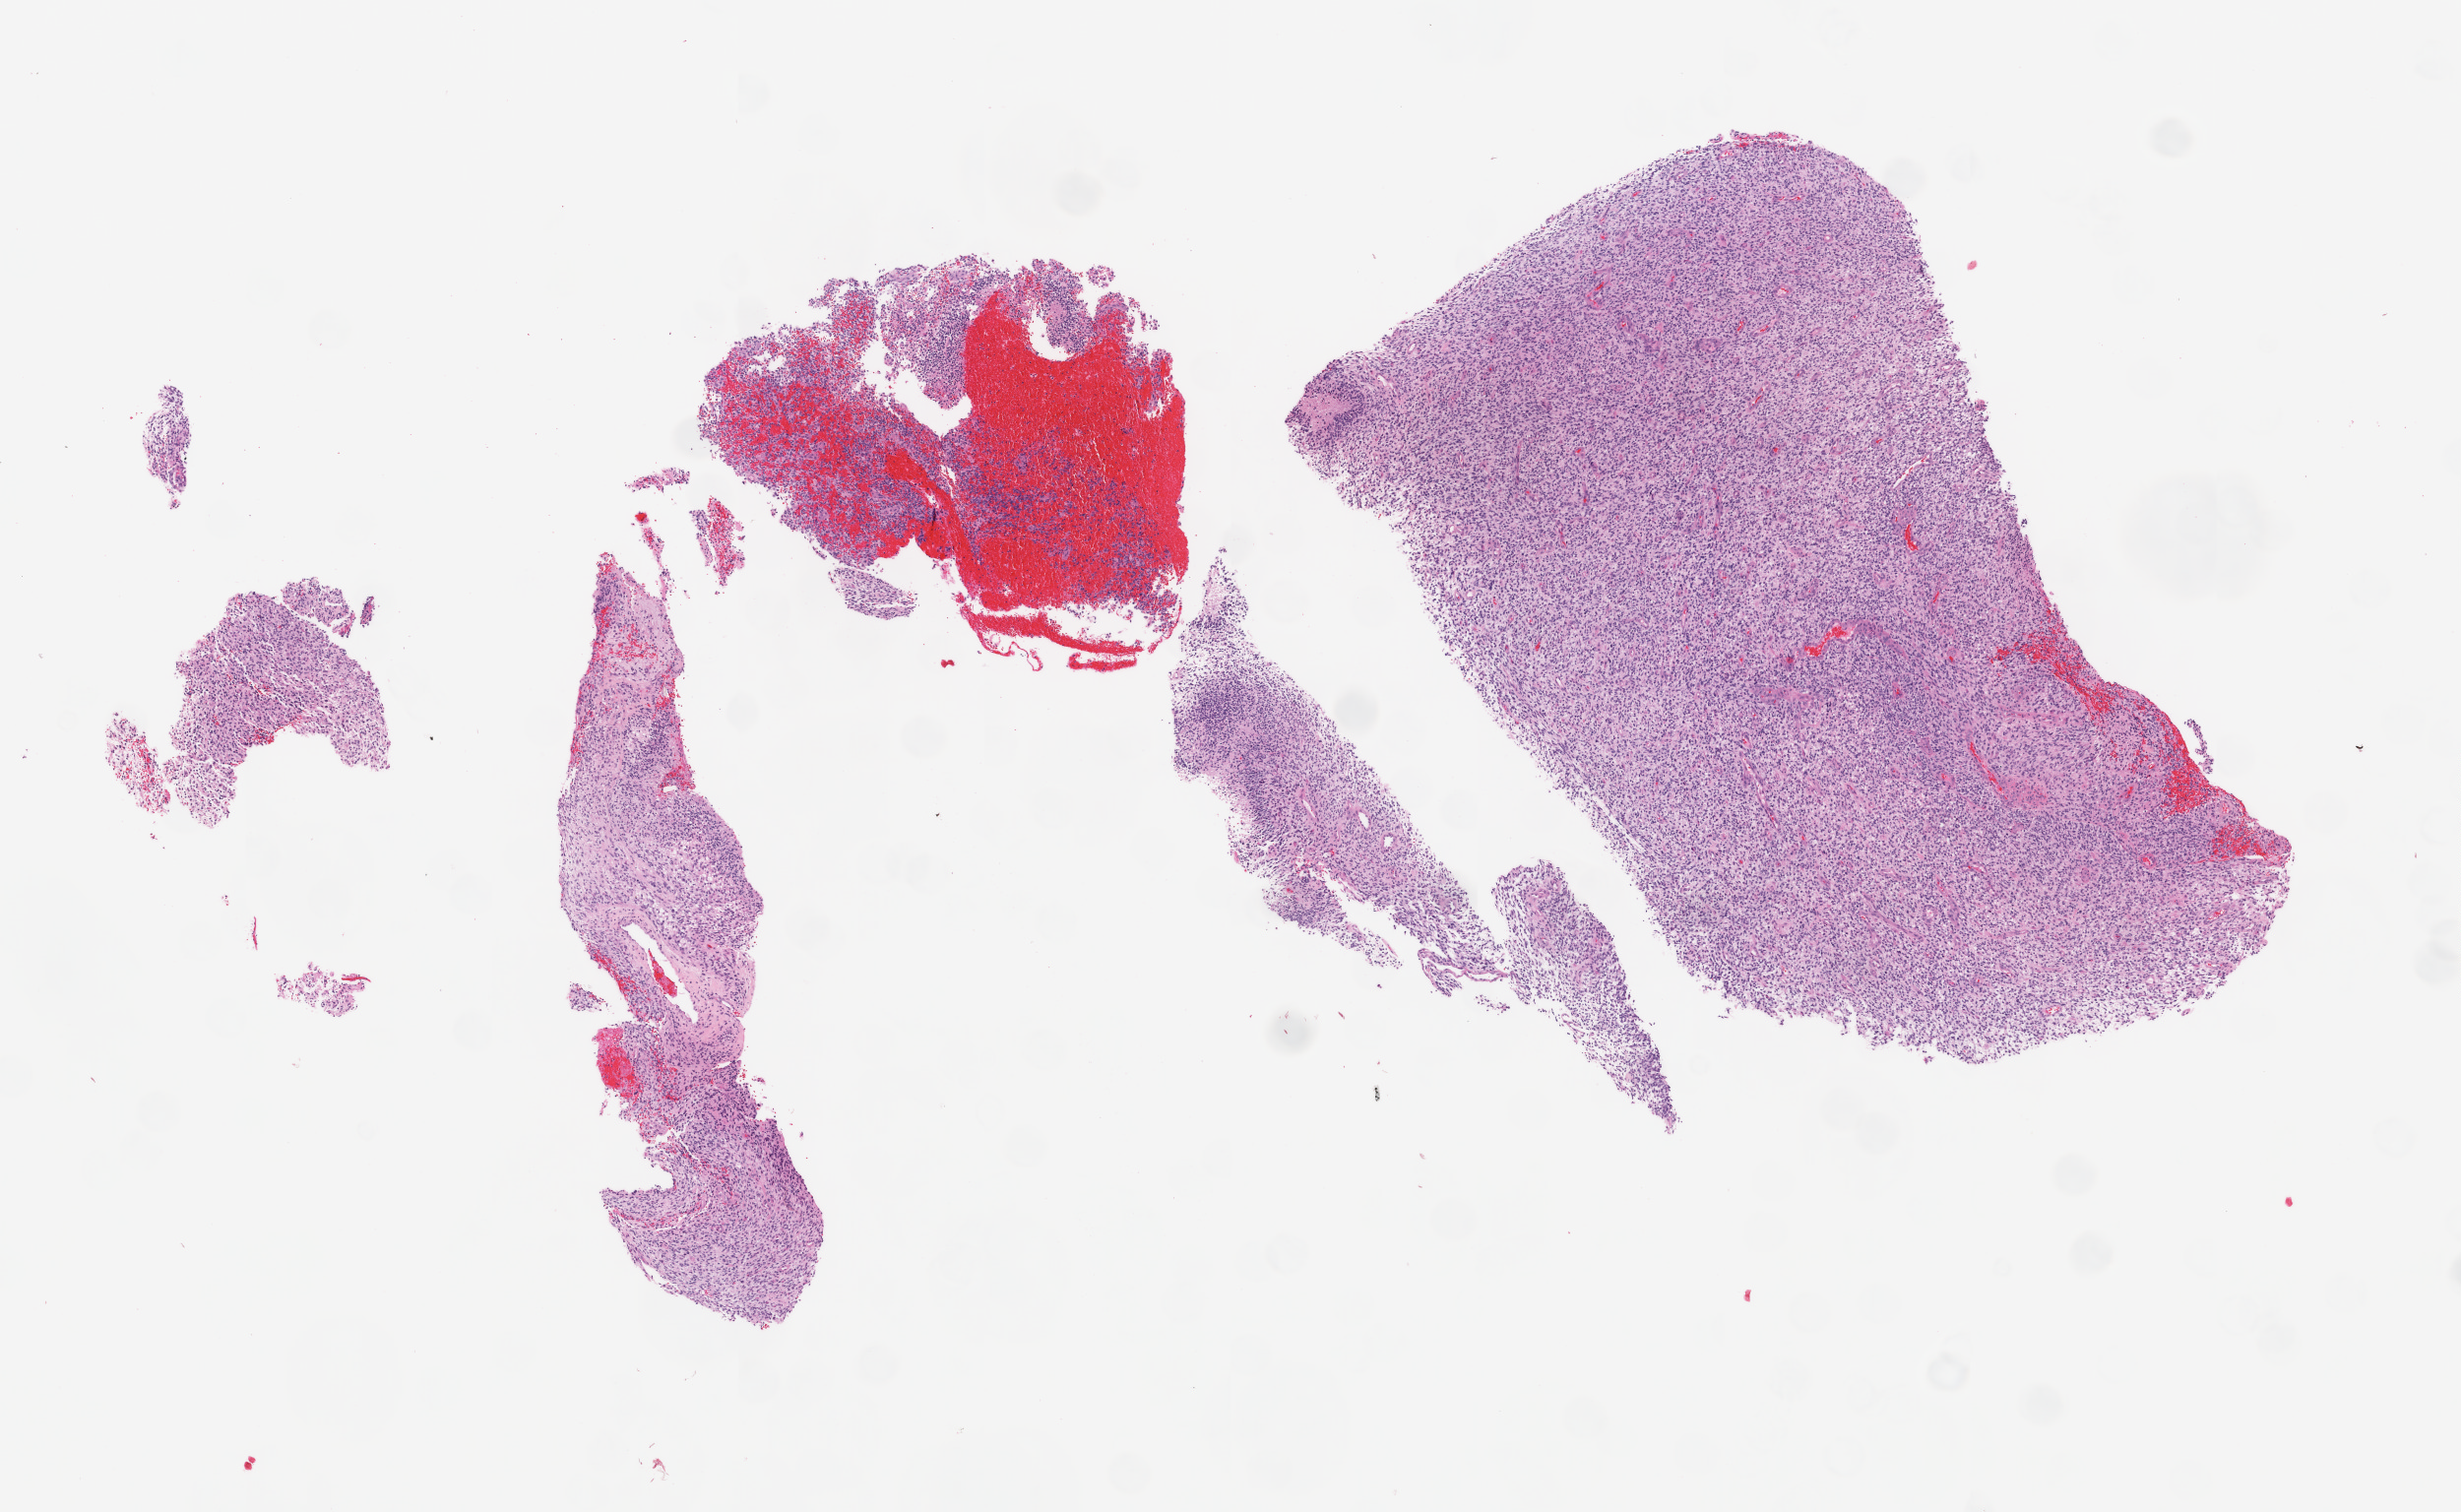
Digitized H&E tissue section (whole slide) — a low-resolution overview of the entire scanned area, about 10.0 x 6.2 mm (slide scanned at 20x); frozen section from the top of the tissue portion; primary tumour sample from the brain. Female, age 66 years at initial diagnosis. Slide review estimates, as recorded: tumour cells 98%, tumour nuclei 85%, normal cells 0%, stromal cells 0%, necrosis 2%.
• diagnosis: Glioblastoma